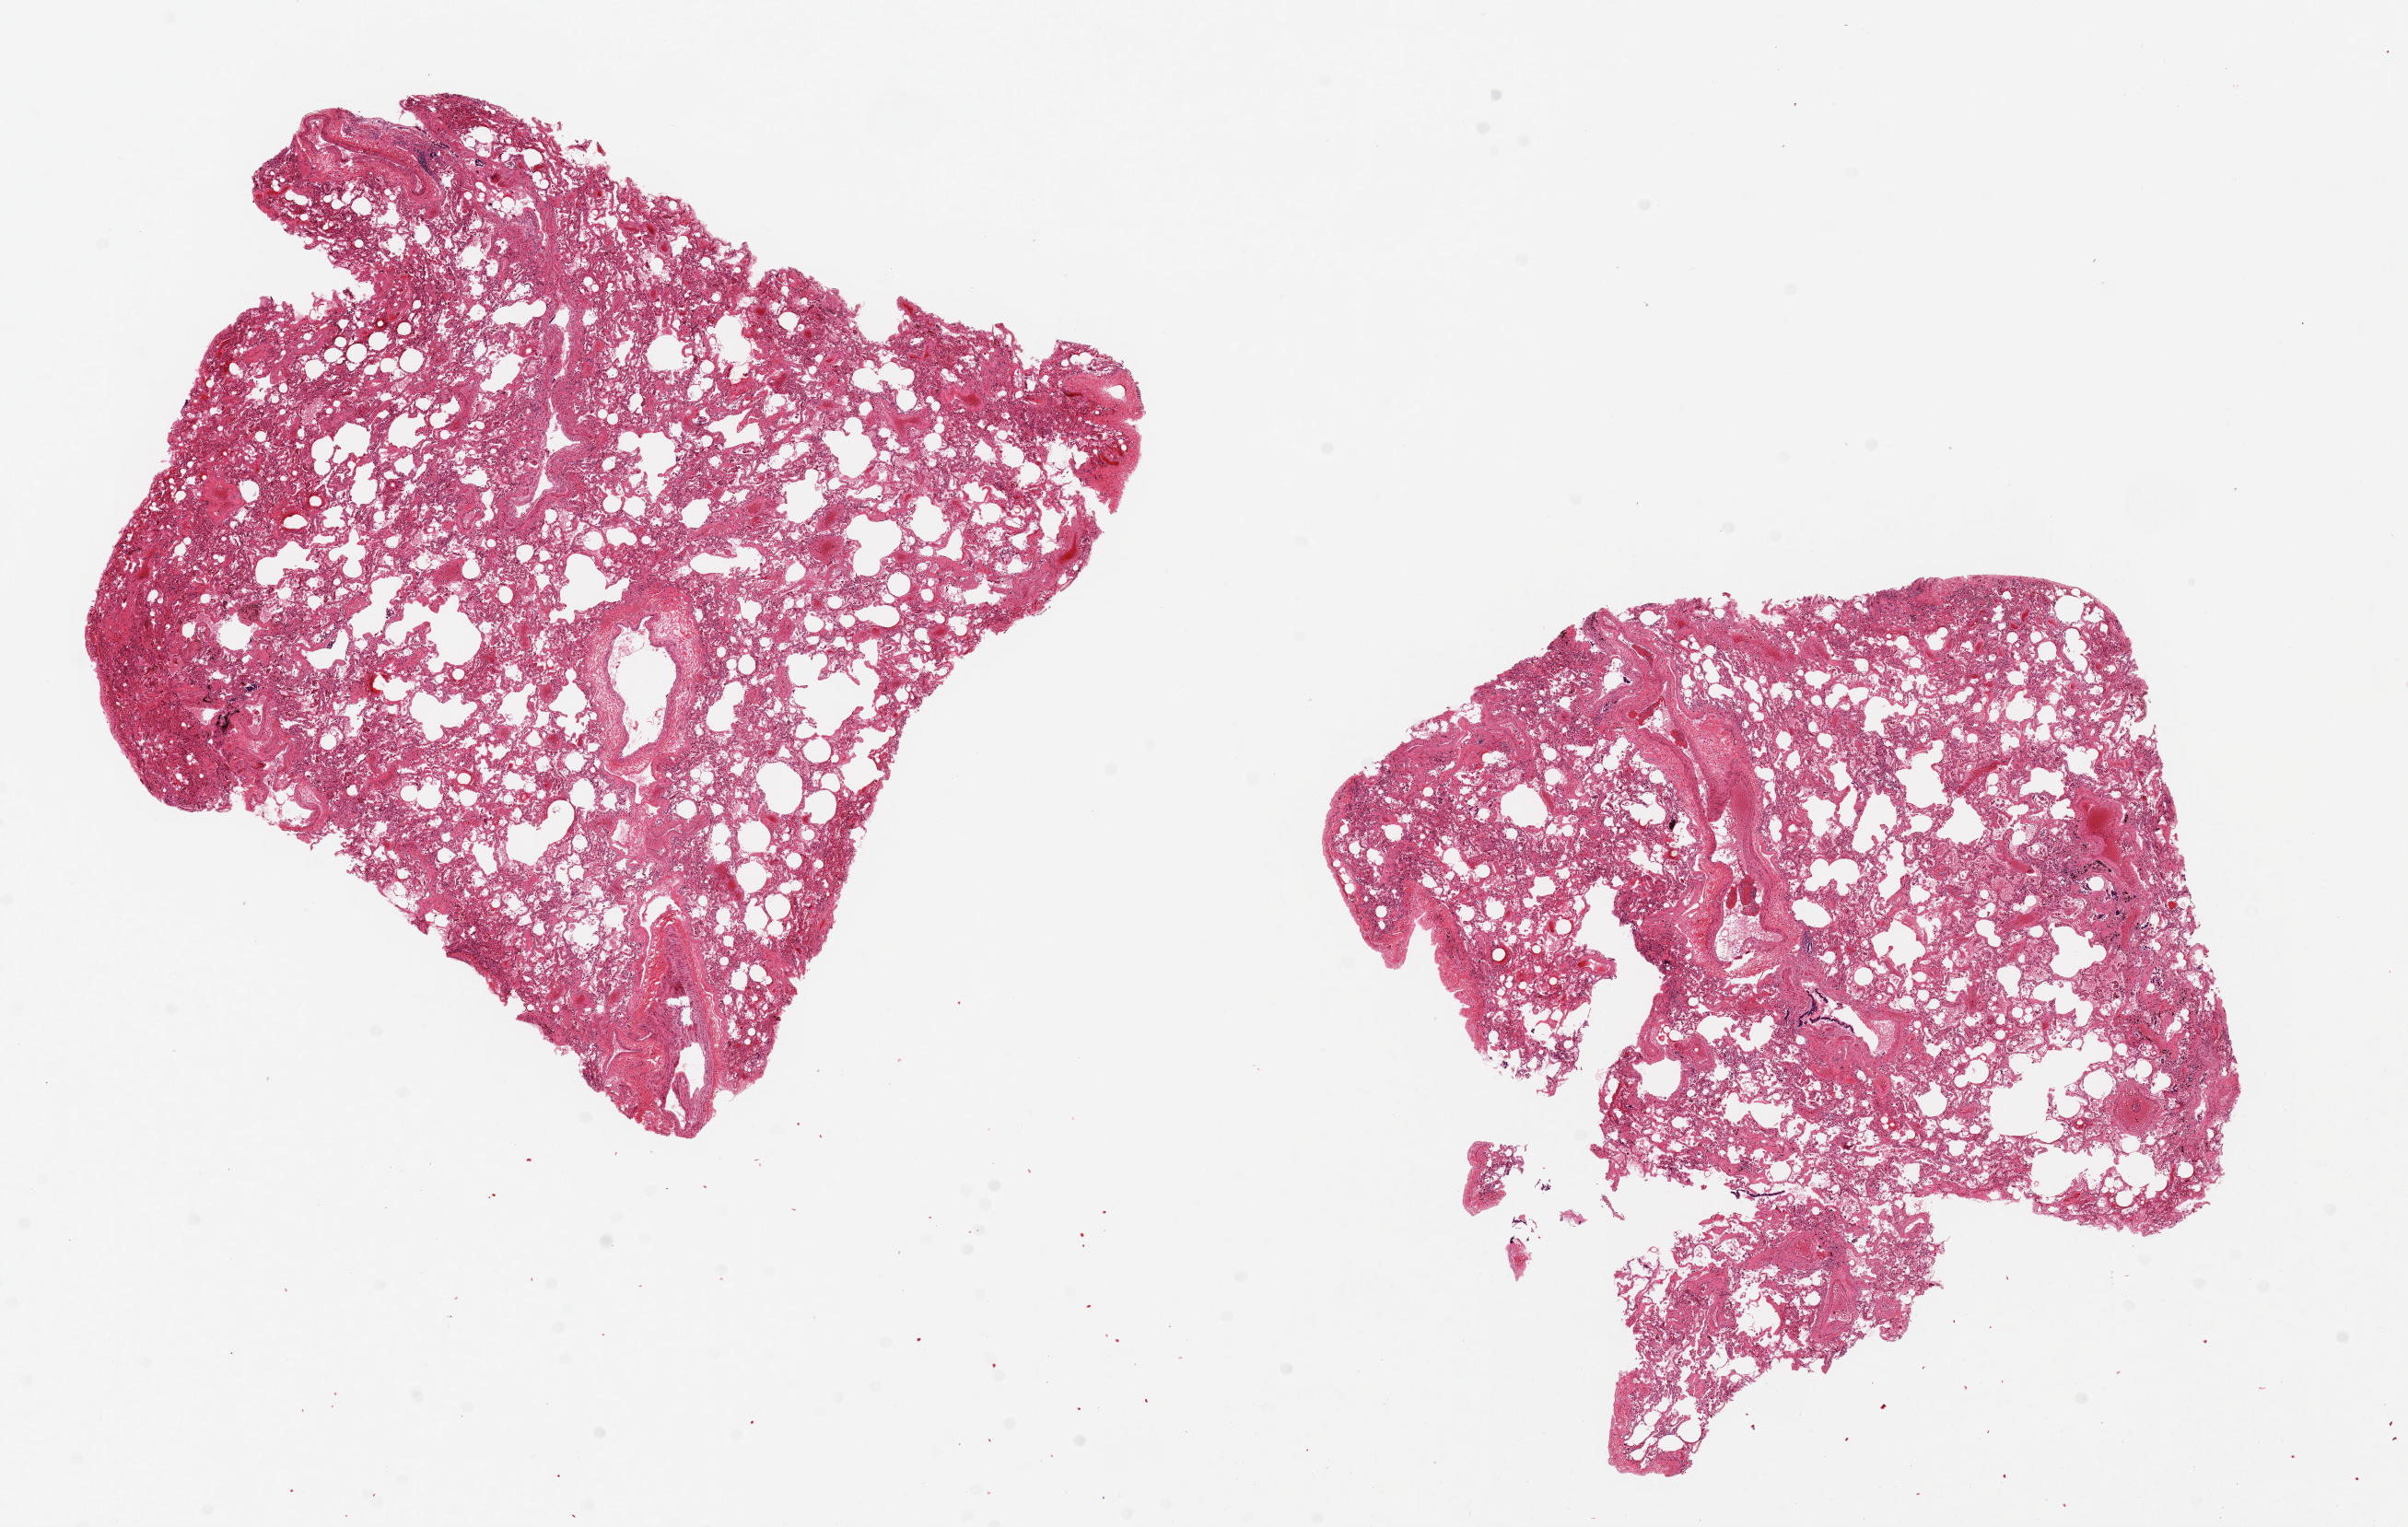
Digitized hematoxylin and eosin (H&E)-stained section — shown as a low-resolution overview of the whole scanned area (about 20.7 x 13.1 mm), PAXgene-fixed paraffin-embedded (PFPE) section, sampled site (target tissue): lung, tissue donor sample. Male donor.
Reviewer comment on this tissue sample: 2 pieces, 8x7 & 7x6mm; moderate vascular and interstitial fibrosis; heart failure cells.